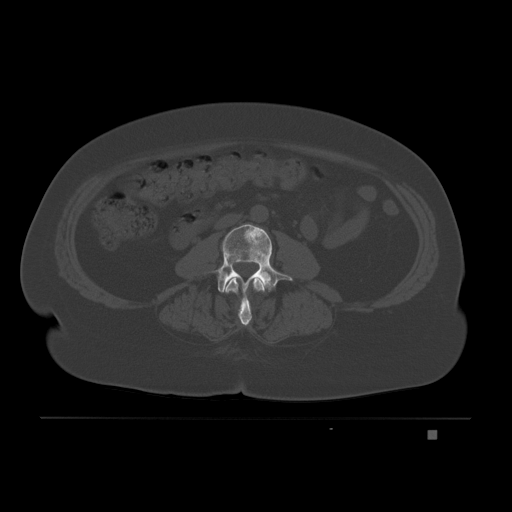
CT including the spine, one axial slice. Position 53 of 221 along the scan axis. Bone window (W 1800 / L 400 HU). 3 mm slice thickness. 512 × 512 image matrix, field of view 474 × 474 mm. Patient: female, 63 years. From the clinical record (not read from this slice): primary cancer: breast.
Structures marked on this image (semi-automatically segmented with operator editing):
- L2 vertebra: bounding box (x1, y1, x2, y2) in pixels: (224, 278, 265, 326)
- L3 vertebra: (202, 224, 293, 303)